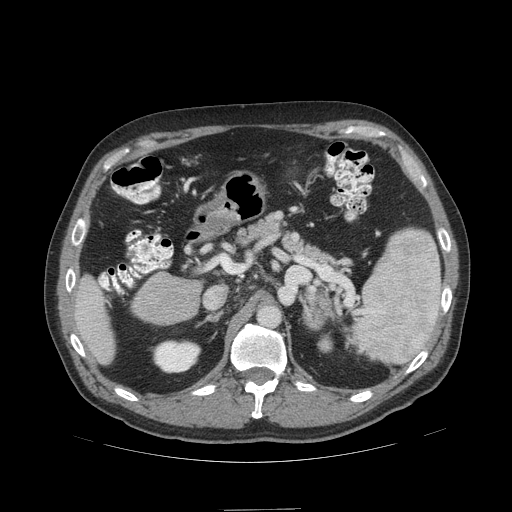
Contrast-enhanced abdominal CT (liver protocol), one axial slice; position 60 of 99 along the scan axis; reconstruction kernel STANDARD; 140 kVp; soft-tissue window (W 400 / L 40 HU); 512 × 512 image matrix, field of view 440 × 440 mm. Case-level facts recorded for this patient, not image findings: diagnosis: hepatocellular carcinoma (patient treated with transarterial chemoembolisation; whether this scan precedes or follows treatment is not stated here); TNM stage (as recorded): Stage-I; Child-Pugh class: A.
Annotated regions visible in this slice (semi-automatically segmented with operator editing):
- liver parenchyma outside the tumour (the mass and vessels are separate outlines, so this box may not span the whole liver): bounding box [x1, y1, x2, y2] px = [72, 274, 116, 364]